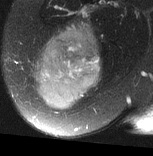
MRI of an extremity soft-tissue mass, one axial slice; position 26 of 77 along the scan axis; T2-weighted fat-saturated; MR volume resampled by the dataset authors to the PET/CT grid (not the native acquisition matrix); 153 × 156 image matrix, field of view 149 × 152 mm. Female patient. From the clinical record (not read from this slice): histological type: synovial sarcoma; grade: intermediate; site of the primary tumour: right buttock.
Outlined on this slice (expert contour drawn on MRI and transferred to this co-registered scan by the dataset authors):
- gross tumour volume including surrounding oedema: bounding box (x1, y1, x2, y2) in pixels: (33, 22, 102, 110)
- gross tumour volume (mass): (33, 27, 102, 110)